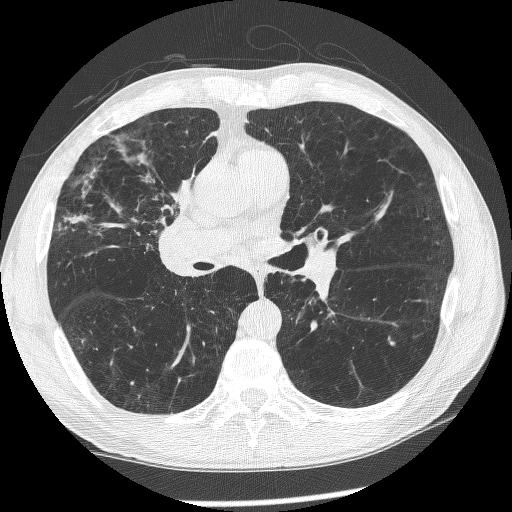
Low-dose screening chest CT, axial slice. Baseline screening round. Lung window (W 1500 / L -600 HU). 1.25 mm slice thickness. Male participant, aged 60 years at enrolment. Current smoker at enrolment.
- Lesion marked by an expert reader, box from (x=146, y=173) to (x=214, y=267) px.
- Screening reader's record for this exam (one nodule recorded; not confirmed to be the boxed lesion): non-calcified nodule or mass ≥4 mm, right upper lobe, 12 × 8 mm, spiculated (stellate) margins, mixed attenuation.
- Participant outcome: lung cancer diagnosed 208 days after this screen — squamous cell carcinoma, NOS, right upper lobe, right middle lobe, right main stem bronchus, poorly differentiated (G3), stage IV (AJCC 6th edition).